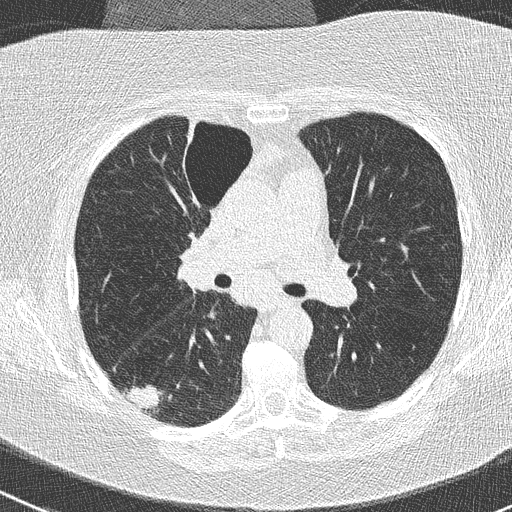
Low-dose screening chest CT, one axial slice. Slice 157 of 261 in the series (ordered by position). 120 kVp. Lung window (W 1500 / L -600 HU). 2 mm slice thickness. 512 × 512 image matrix, field of view 310 × 310 mm.
Annotated regions visible in this slice (expert manual segmentation):
- lesion 1 (tumor, lower lobe of right lung): bounding box (x1, y1, x2, y2) in pixels: (125, 385, 163, 411)